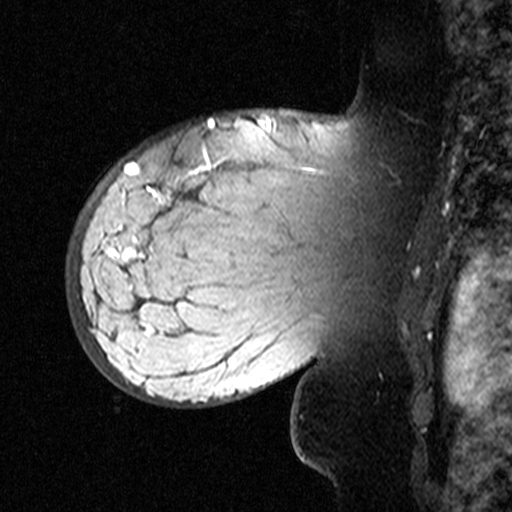
Breast MRI (dynamic contrast-enhanced), one sagittal slice. Position 33 of 44 along the scan axis. Dynamic contrast-enhanced study with each time point stored as its own series, time point 2 of 3 at this slice position (early post-contrast, ordered by acquisition time). 1.5 T. TE 4.5 ms, TR 11 ms. 3 mm slice thickness. 512 × 512 image matrix. Patient: female, 53 years. Case-level facts recorded for this patient, not image findings: setting: breast cancer imaged before/during neoadjuvant chemotherapy; receptor status: HR-positive, HER2-negative.
Outlined on this slice (semi-automatically segmented with operator editing):
- analysis volume of interest (the breast-tissue region the enhancement analysis was run in; not a lesion): bounding box <76,140,311,353> (left, top, right, bottom; pixels)
- tumour enhancement mask (voxels above the 90 % enhancement threshold inside the analysis volume of interest): <111,149,212,333>